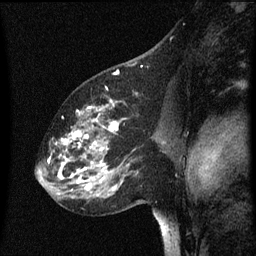
Breast MRI (dynamic contrast-enhanced), one sagittal slice. Position 38 of 60 along the scan axis. Dynamic contrast-enhanced series, image 2 of 3 at this slice position (ordered by acquisition). 1.5 T. TE 4.2 ms, TR 8 ms. 2 mm slice thickness. 256 × 256 image matrix. Patient: female, 60 years.
Structures marked on this image (semi-automatically segmented with operator editing):
- analysis volume of interest (the breast-tissue region the enhancement analysis was run in; not a lesion): box from (x=49, y=100) to (x=158, y=197) px
- tumour enhancement mask (voxels above the 70 % enhancement threshold inside the analysis volume of interest): (x=57, y=100)–(x=119, y=191)